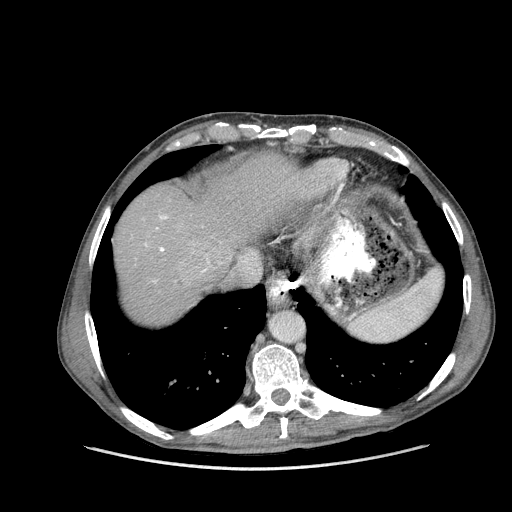
Contrast-enhanced abdominal CT (liver protocol), one axial slice; slice 131 of 162 in the series (ordered by position); reconstruction kernel STANDARD; 100 kVp; soft-tissue window (W 400 / L 40 HU); 2.5 mm slice thickness; 512 × 512 image matrix, field of view 400 × 400 mm. Case-level facts recorded for this patient, not image findings: diagnosis: hepatocellular carcinoma (patient treated with transarterial chemoembolisation; whether this scan precedes or follows treatment is not stated here); TNM stage (as recorded): Stage-IIIA; Child-Pugh class: A; tumour nodularity: multinodular; tumour size: 9.9 cm.
Annotated regions visible in this slice (semi-automatic segmentation, software-assisted and operator-edited):
- abdominal aorta: bounding box (x1, y1, x2, y2) in pixels: (272, 312, 303, 343)
- liver parenchyma outside the tumour (the mass and vessels are separate outlines, so this box may not span the whole liver): (114, 154, 336, 324)
- liver vessels: (145, 215, 209, 283)